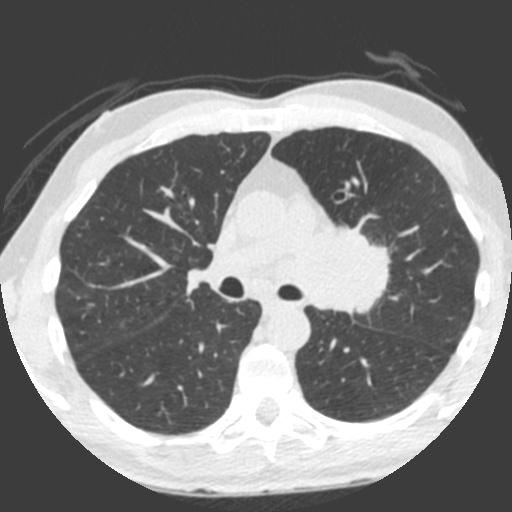
Chest CT (low-dose screening protocol), one axial image, third screening round (two years after baseline), lung window (W 1500 / L -600 HU), 2 mm slice thickness, slice 136 of 212 in the series, 512 × 512 image matrix, field of view 315 × 315 mm. Male, age 55 years at enrolment.
Expert-annotated lung lesion, bounding box <309,218,397,324> (left, top, right, bottom; pixels). Screening reader's record for this exam (one nodule recorded; not confirmed to be the boxed lesion): non-calcified nodule or mass ≥4 mm, left upper lobe, 49 × 29 mm, spiculated (stellate) margins, soft tissue attenuation, pre-existing on the prior screen: yes; interval growth: yes.